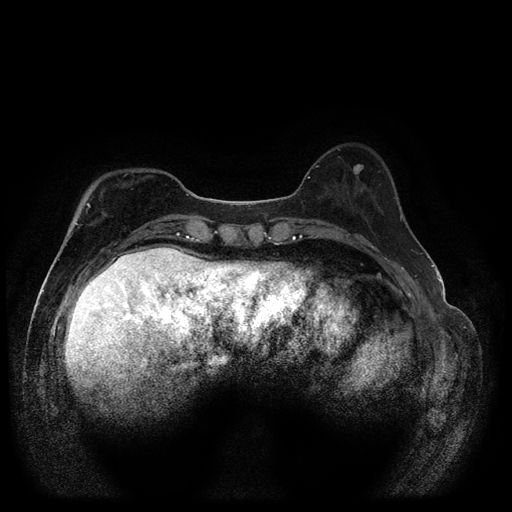
Breast MRI (dynamic contrast-enhanced, multi-phase), one axial slice; position 32 of 116 along the scan axis; dynamic contrast-enhanced series, time point 2 of 5 at this slice position (early post-contrast); 1.5 T; TE 2.6 ms, TR 5.4 ms; 2 mm slice thickness; 512 × 512 image matrix, field of view 340 × 340 mm. Patient: female, 51 years.
Outlined on this slice (semi-automatically segmented with operator editing):
- breast lesion (labelled benign in the annotation): bounding box (x1, y1, x2, y2) in pixels: (353, 164, 364, 177)